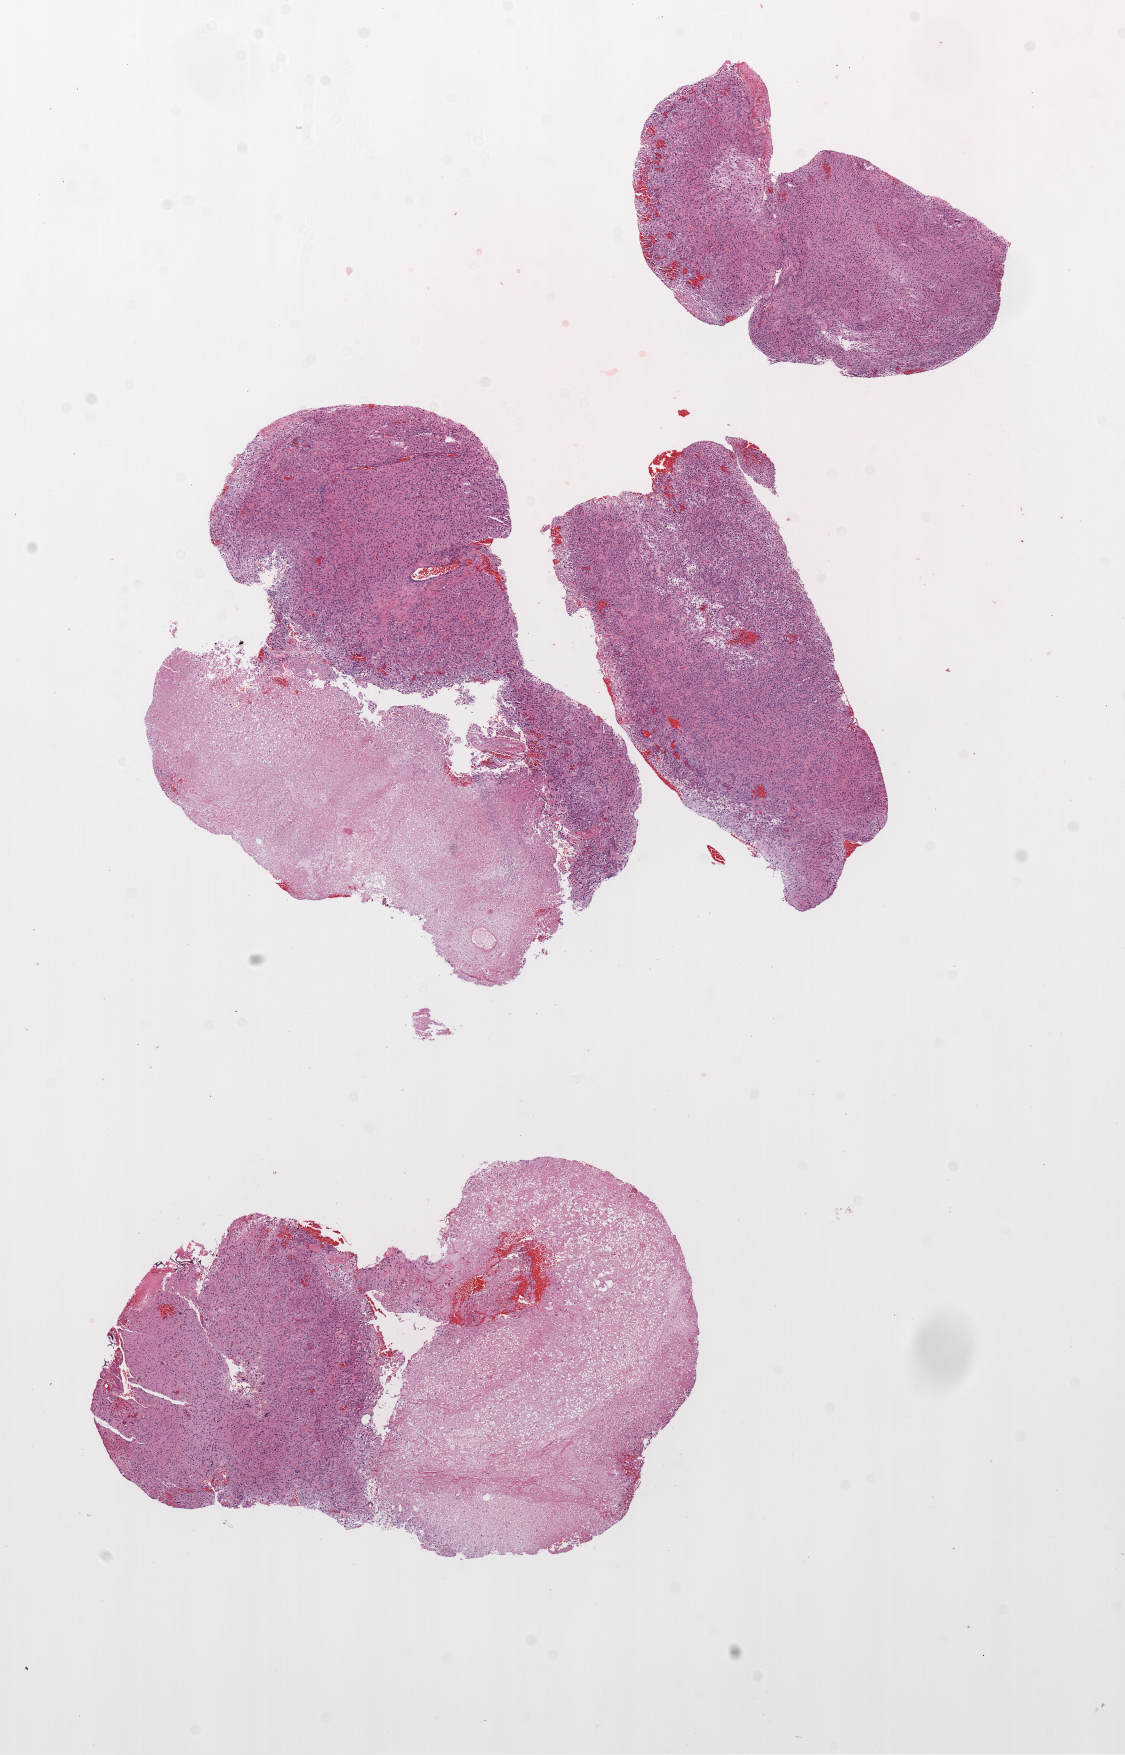
Digitized H&E-stained tissue section (whole slide) — a low-resolution overview of the entire scanned area, about 9.0 x 14.1 mm (from a 20x scan), formalin-fixed paraffin-embedded (FFPE) diagnostic section, sample: primary tumour, brain. Male patient; age at initial diagnosis 69 years.
Histologic diagnosis: Glioblastoma.